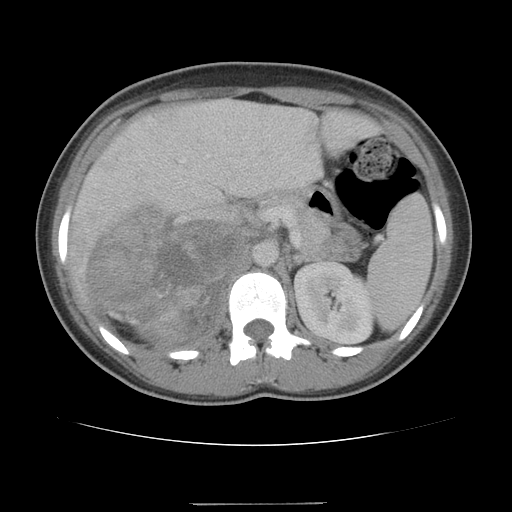
Contrast-enhanced abdominal CT, one axial slice; soft-tissue window (W 400 / L 40 HU); 512 × 512 image matrix. Patient: female, 21 years. Case-level facts recorded for this patient, not image findings: diagnosis: adrenocortical carcinoma; tumour side: right adrenal; tumour size at pathology: 15.5 cm; Ki-67 index: 26 %; stage (as recorded): 3.
Annotated regions visible in this slice (semi-automatic segmentation, software-assisted and operator-edited):
- mass: bounding box <88,211,249,344> (left, top, right, bottom; pixels)